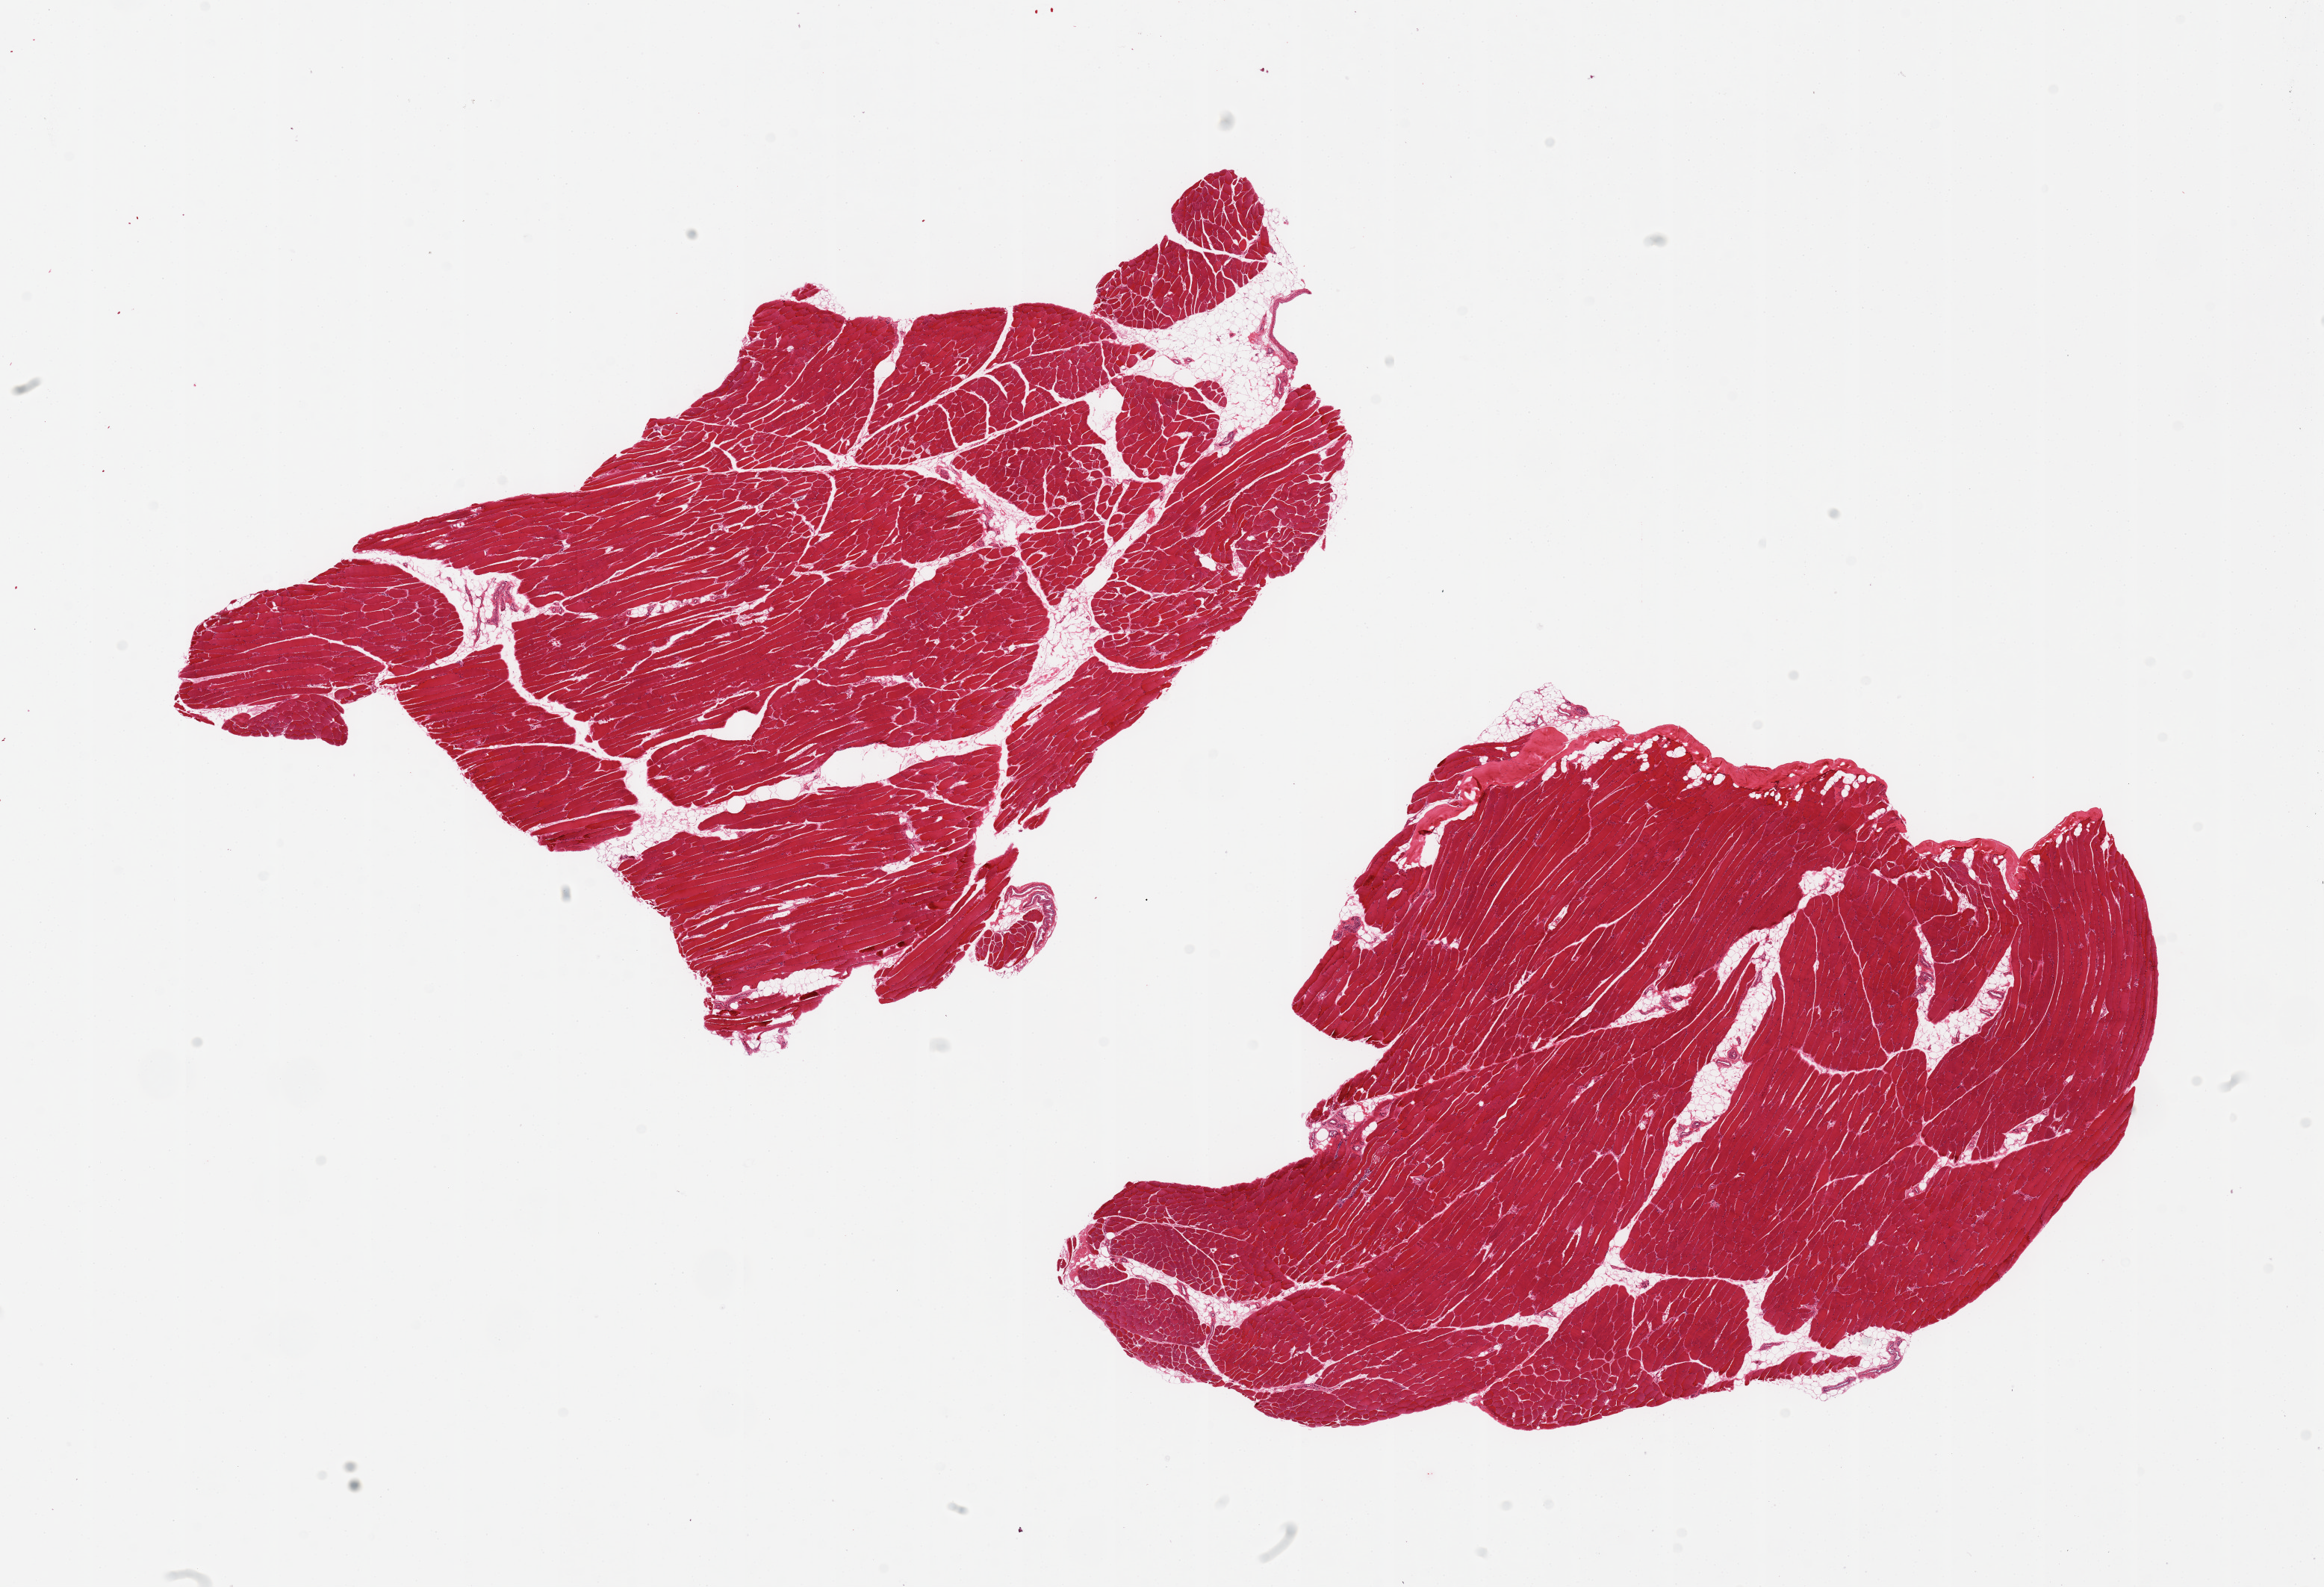
Whole-slide image, haematoxylin and eosin stain — shown as a low-resolution overview of the whole scanned area (about 24.6 x 16.8 mm). PAXgene-fixed, paraffin-embedded tissue. Sampled site (target tissue): skeletal muscle. Tissue donor sample. Donor: male.
* pathologist's review note for this sample: 2 pieces, 10-20% interstitial fat